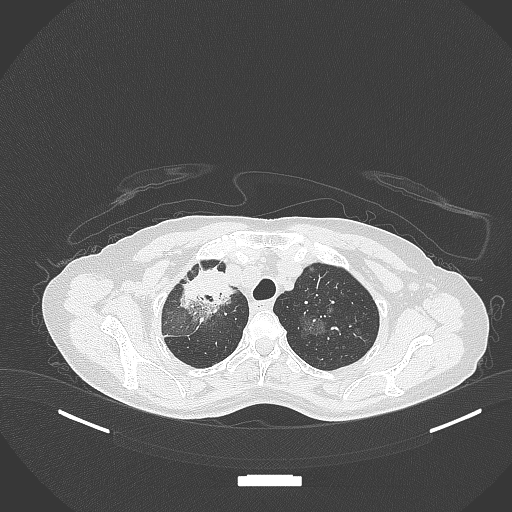
Chest CT, one axial slice; slice 271 of 284 in the series (ordered by position); lung window (W 1500 / L -600 HU); 512 × 512 image matrix, field of view 400 × 400 mm. Patient: female, 59 years. From the clinical record (not read from this slice): clinical TNM (as recorded): T3 N0 M0; histopathological grade: G1.
Outlined on this slice (bounding box drawn by a radiologist):
- lung tumour (recorded histology: adenocarcinoma): bounding box [x1, y1, x2, y2] px = [178, 268, 235, 323]